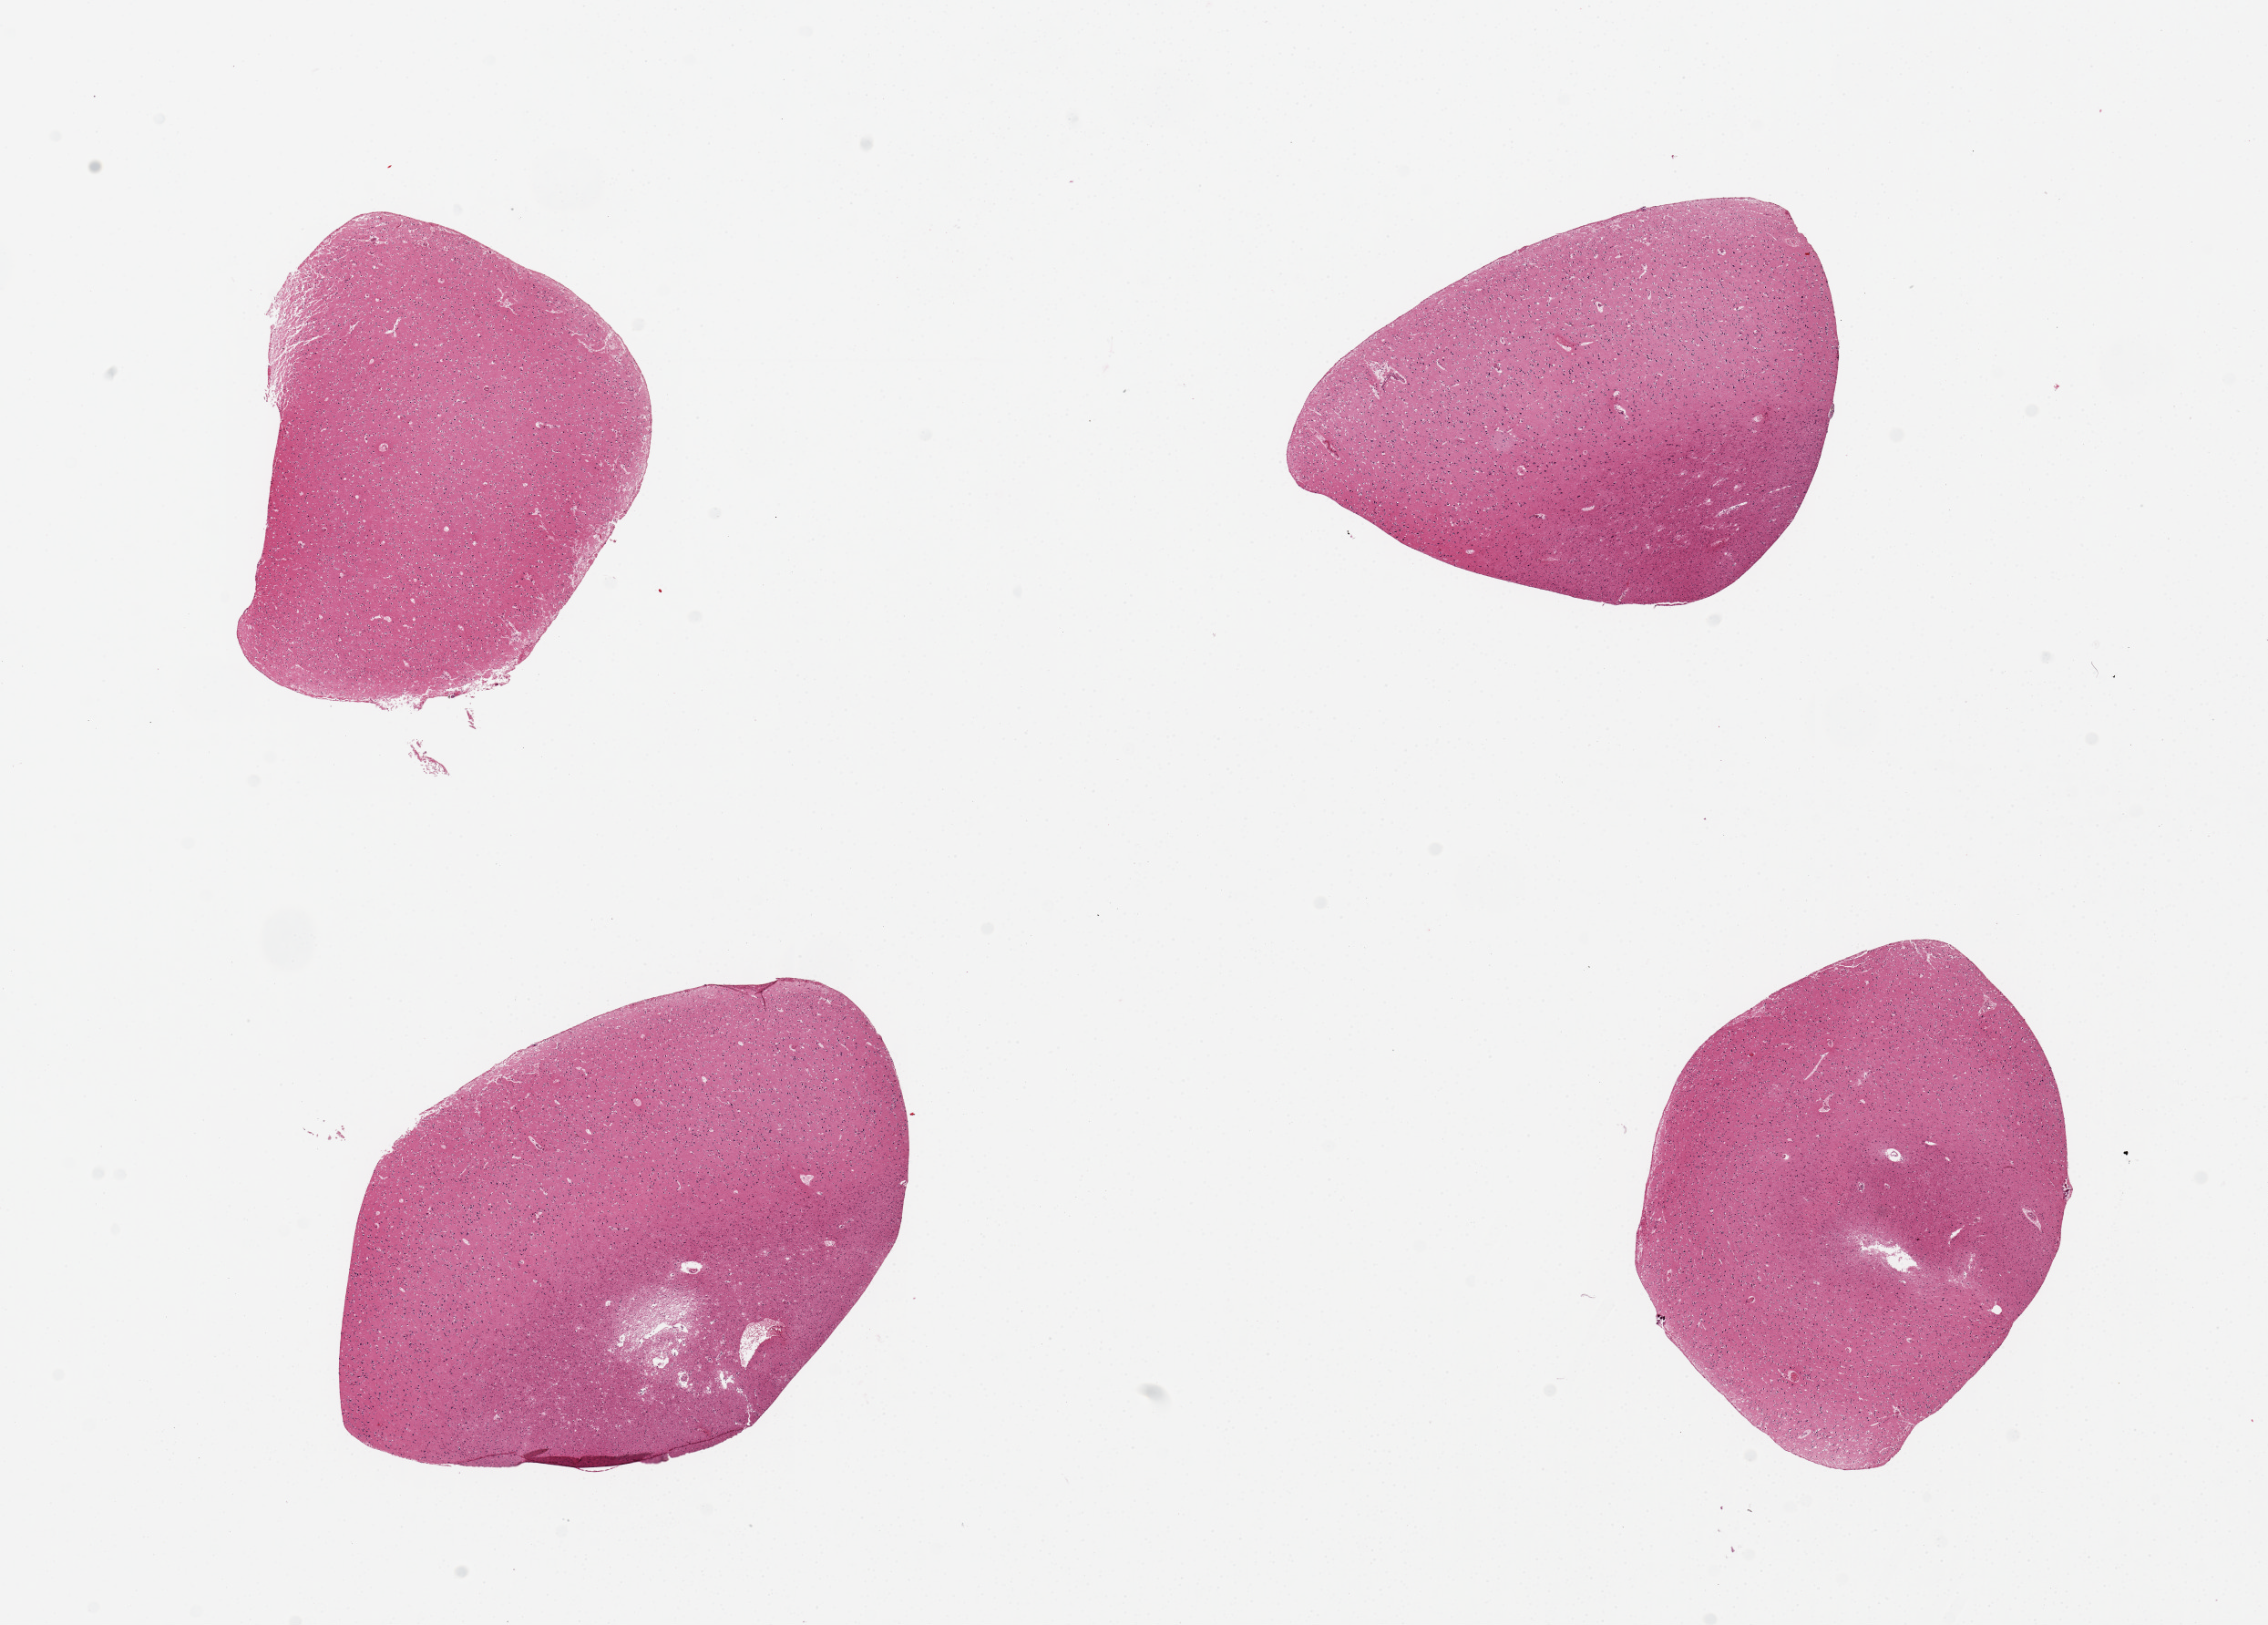
Hematoxylin and eosin (H&E) whole-slide image — low-resolution overview of the scanned area, about 19.7 x 14.1 mm (from a 20x scan), PAXgene-fixed paraffin-embedded (PFPE) section, sampled site (target tissue): cerebral cortex, tissue donor sample. Donor: male.
* reviewer comment on this tissue sample: 4 pieces